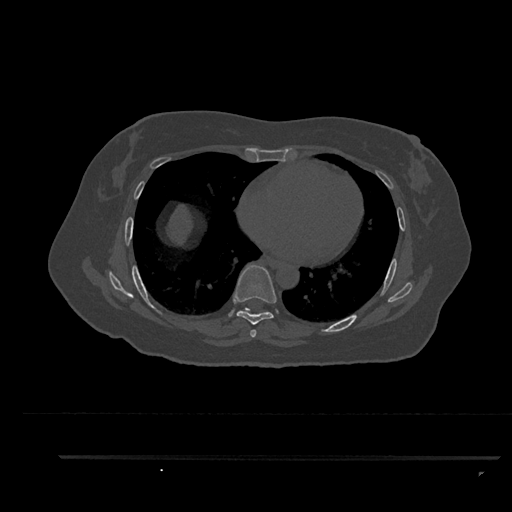
CT including the spine, one axial slice. Slice 502 of 797 in the series (ordered by position). Reconstruction kernel Br40s/3. 120 kVp. Bone window (W 1800 / L 400 HU). 0.5 mm slice thickness. 512 × 512 image matrix. Patient: female, 44 years. Case-level facts recorded for this patient, not image findings: primary cancer: renal; vertebrae with lytic lesions (as recorded): L1.
Outlined on this slice (semi-automatic segmentation, software-assisted and operator-edited):
- T6 vertebra: bounding box [x1, y1, x2, y2] px = [251, 330, 257, 338]
- T7 vertebra: [233, 265, 276, 336]
- T8 vertebra: [240, 308, 267, 314]